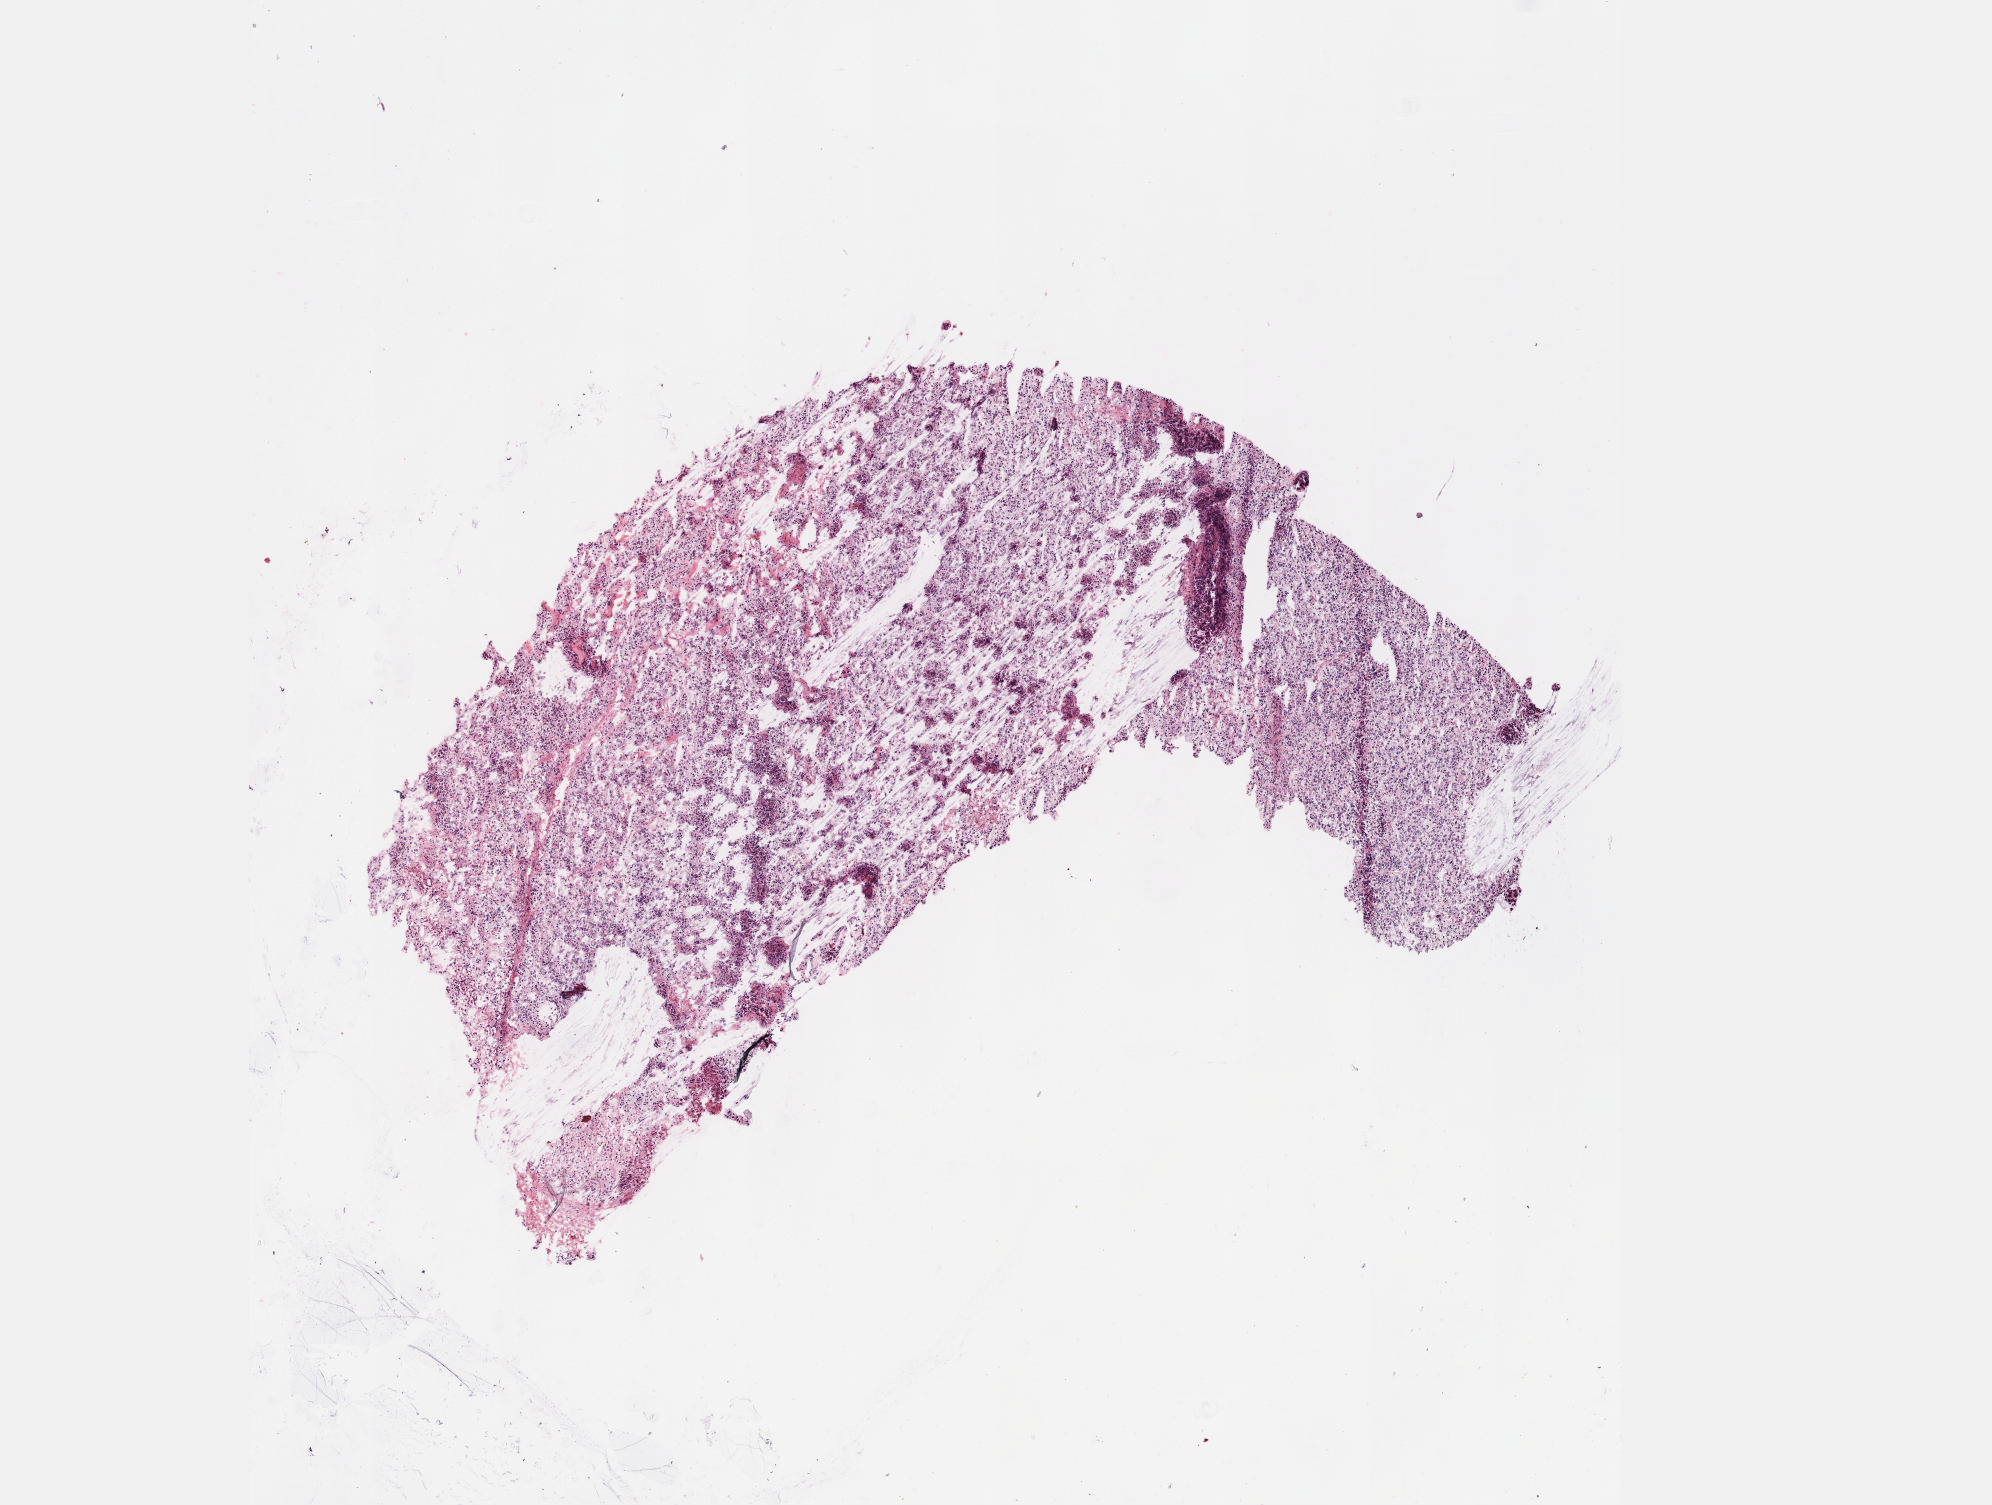
Whole-slide histology image, H&E — a low-resolution overview of the entire scanned area, about 8.0 x 6.1 mm, formalin-fixed paraffin-embedded (FFPE) diagnostic section, primary tumour sample from the adrenal gland. Female patient; age at initial diagnosis 65 years.
- diagnosis: Pheochromocytoma, malignant